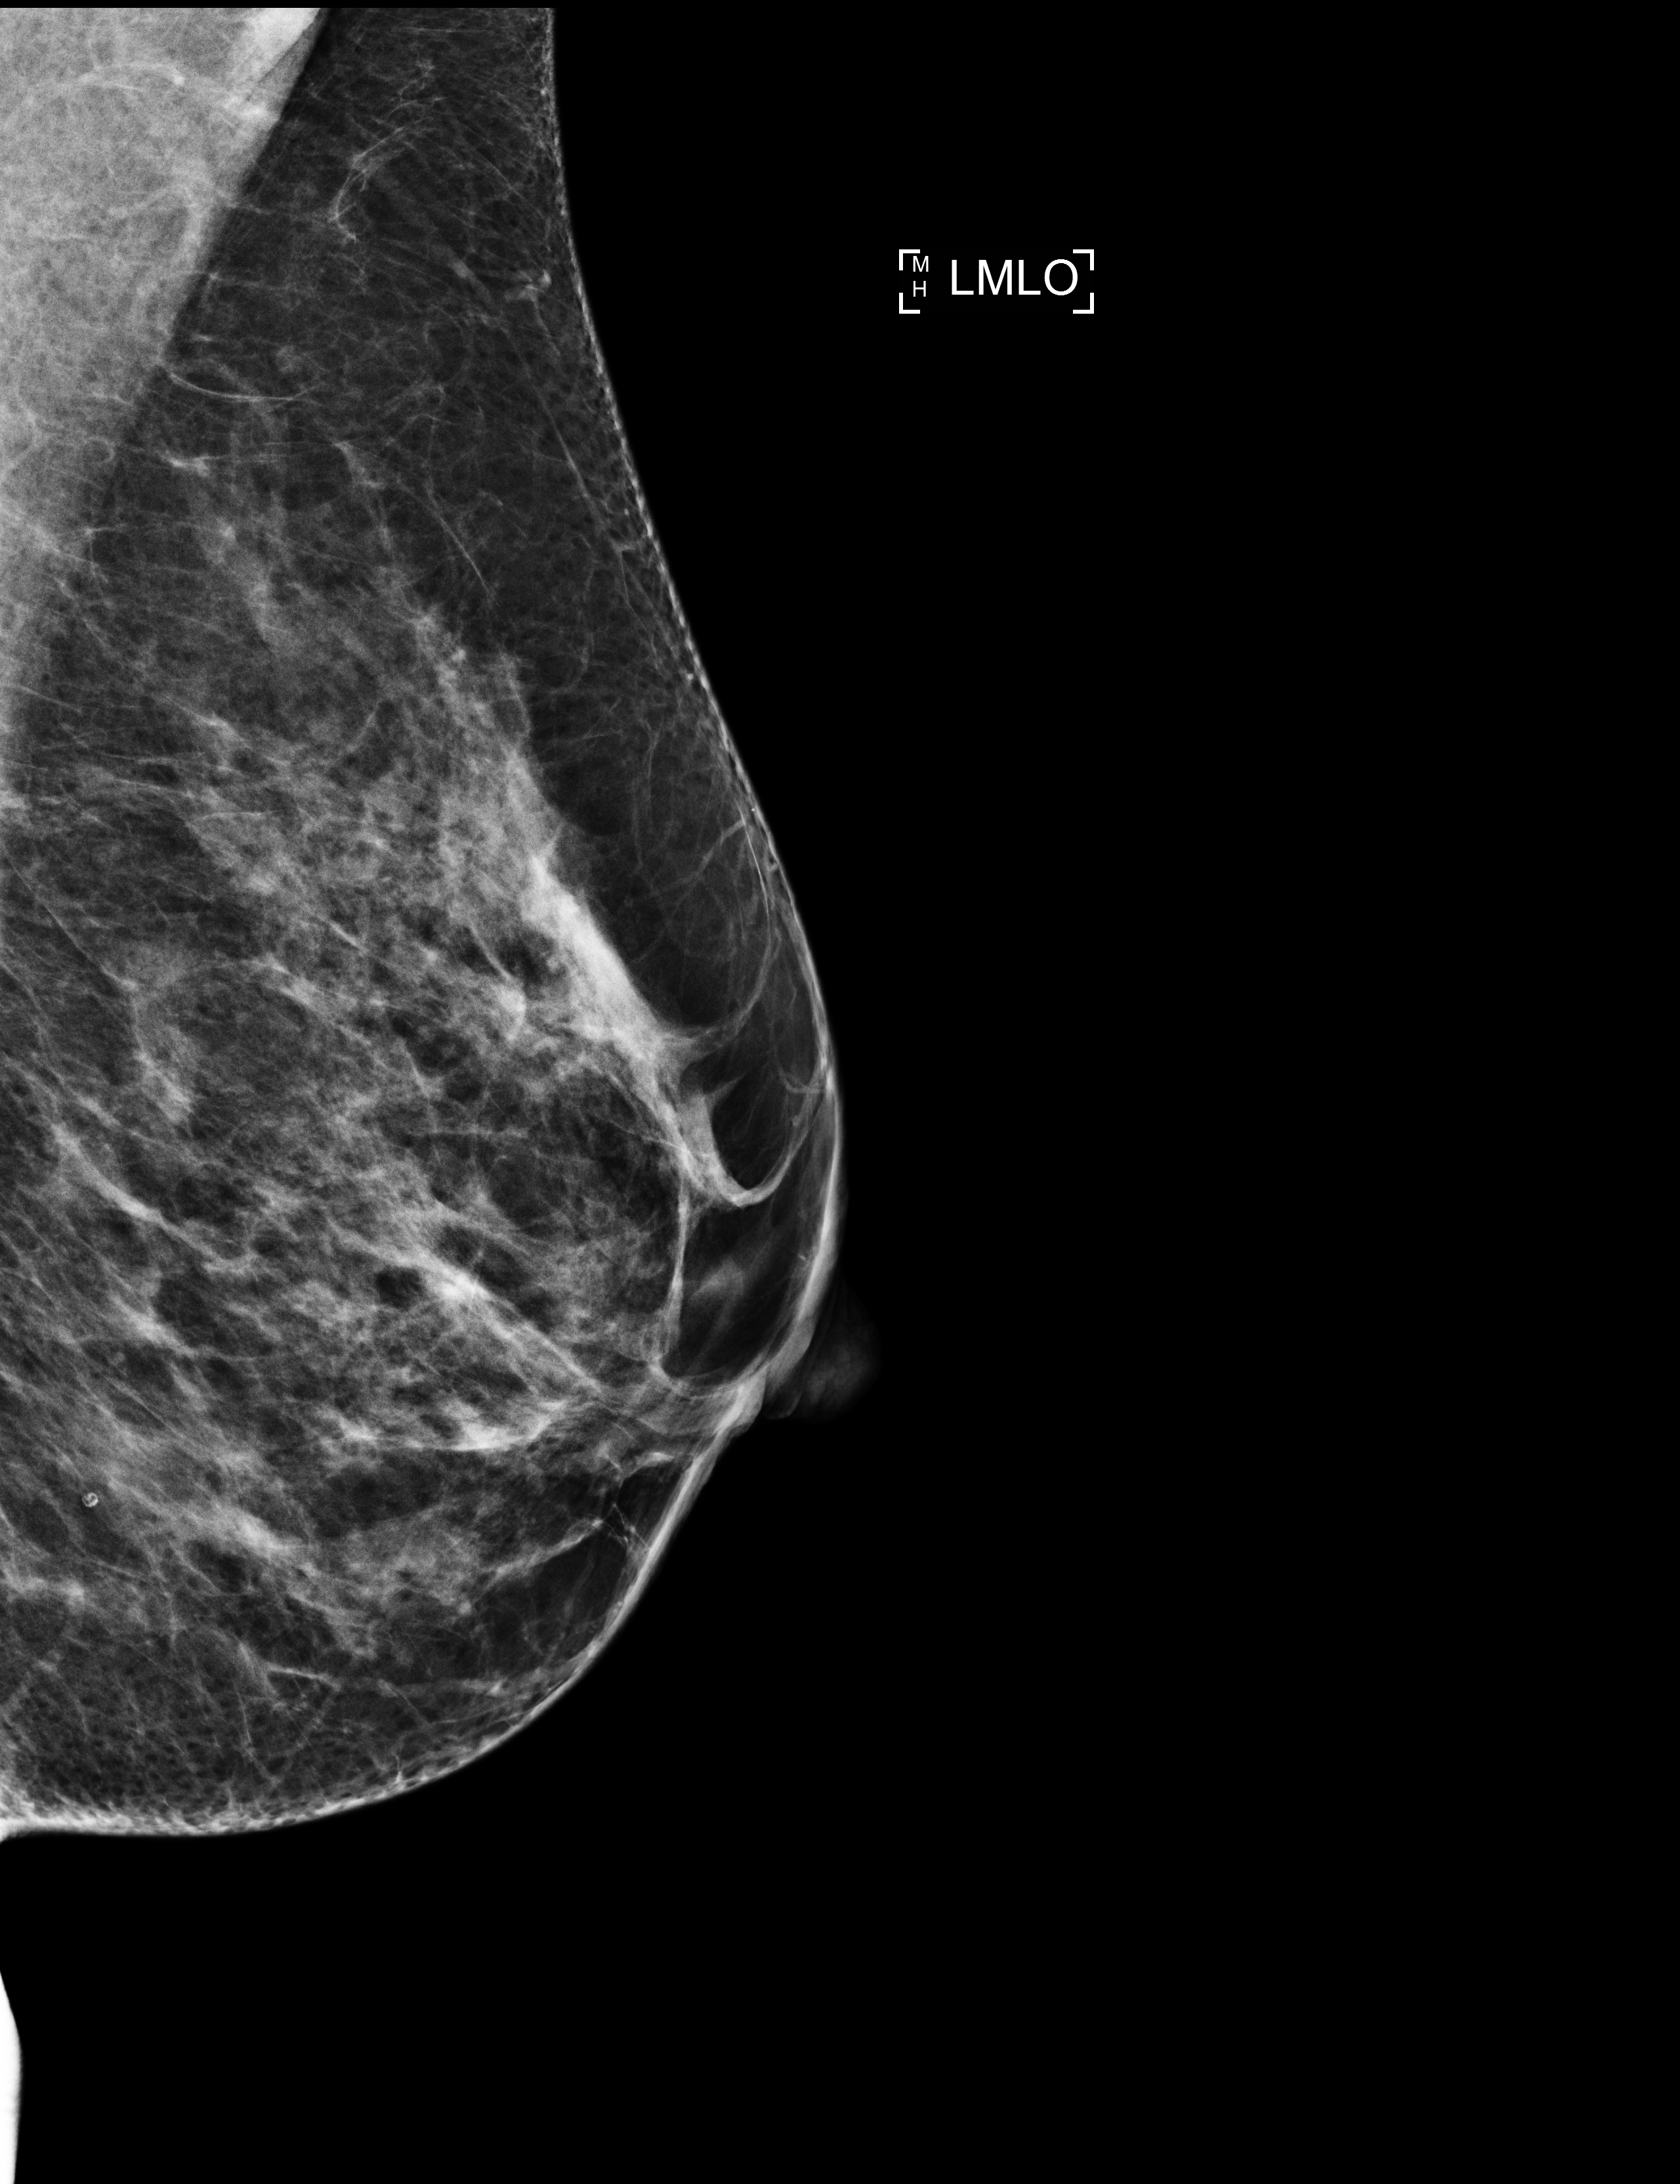
Full-field digital mammogram (FFDM), left breast, mediolateral oblique (MLO) view, screening examination. Patient: female, 51 years.
Breast density at the screening exam (both breasts): heterogeneously dense (BI-RADS density category c). Final BI-RADS assessment for this screening round (tomosynthesis exam, both breasts): category 1. Recall: no recall after this screen.